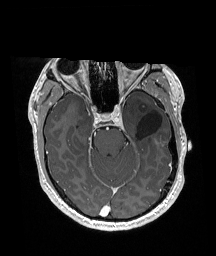
Brain MRI from a brain-tumour surgery series, one axial slice; slice 116 of 192 in the series (ordered by position); T1-weighted post-contrast; 1 mm slice thickness; 216 × 256 image matrix, field of view 211 × 250 mm. From the clinical record (not read from this slice): histopathology: Glioneuronal tumor; WHO grade: 2; tumour location: Left Superior Temporal Gyrus.
Structures marked on this image (outlined manually by an expert reader):
- previous resection cavity: bounding box <137,110,162,139> (left, top, right, bottom; pixels)
- tumour: <142,105,146,108>